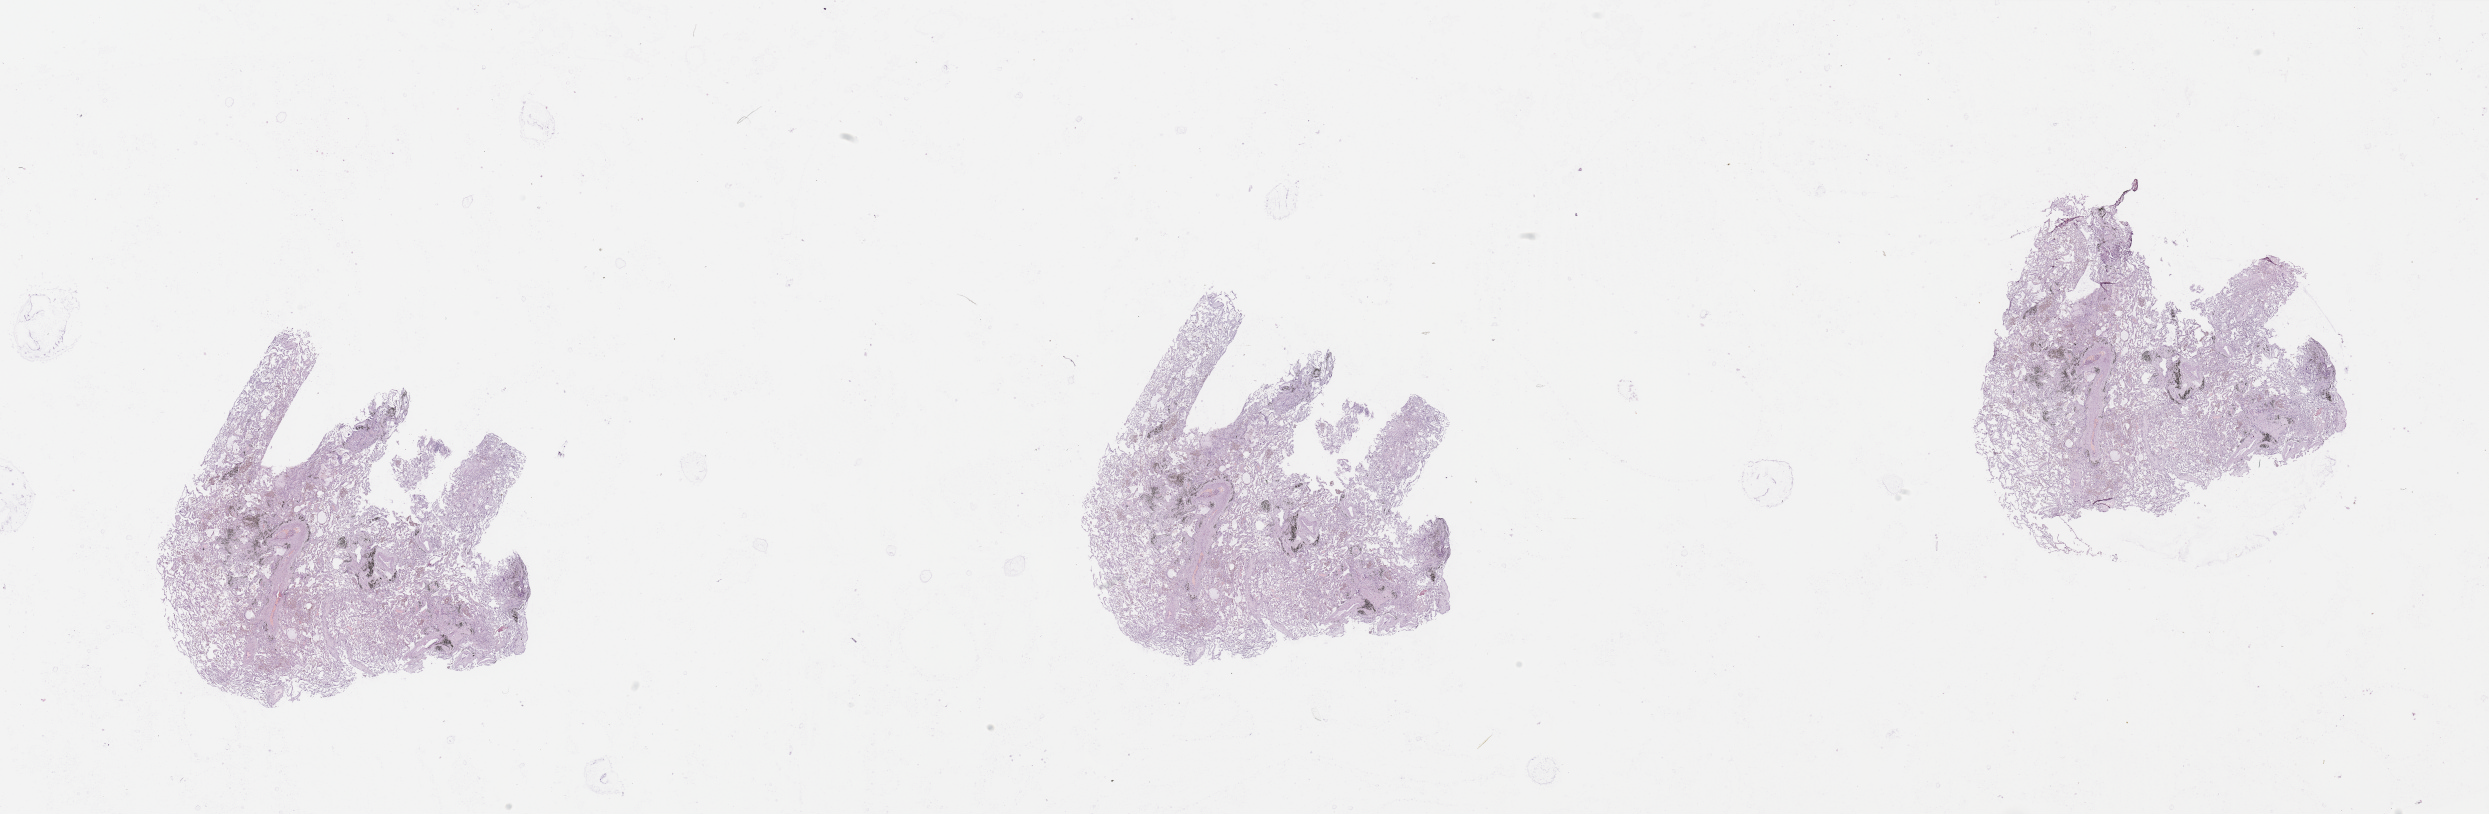
Digitized H&E tissue section (whole slide), whole scanned area (about 39.4 x 12.9 mm) shown as a low-resolution overview; normal (non-tumour) tissue sample, sampled site: lung. Patient: male, age 51 years.
This section: normal (non-tumour) tissue from the same patient. Patient diagnosis: Squamous cell carcinoma, NOS.